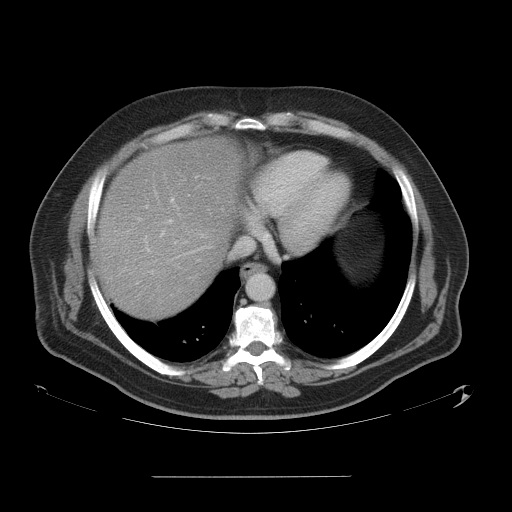
Contrast-enhanced abdominal CT, one axial slice; slice 49 of 58 in the series (ordered by position); 120 kVp; intravenous contrast given; soft-tissue window (W 400 / L 40 HU); 512 × 512 image matrix, field of view 480 × 480 mm. Male patient, age 63 years. Case-level facts recorded for this patient, not image findings: diagnosis: colorectal cancer liver metastases, imaged before liver resection; multiple liver metastases: no; largest metastasis: 4.2 cm.
Annotated regions visible in this slice (outlined manually by an expert reader):
- hepatic veins: bounding box [x1, y1, x2, y2] px = [138, 218, 246, 268]
- liver: [98, 138, 239, 320]
- planned liver remnant (the part of the liver to remain after resection): [98, 208, 222, 320]
- portal vein (with intrahepatic branches): [147, 176, 198, 251]